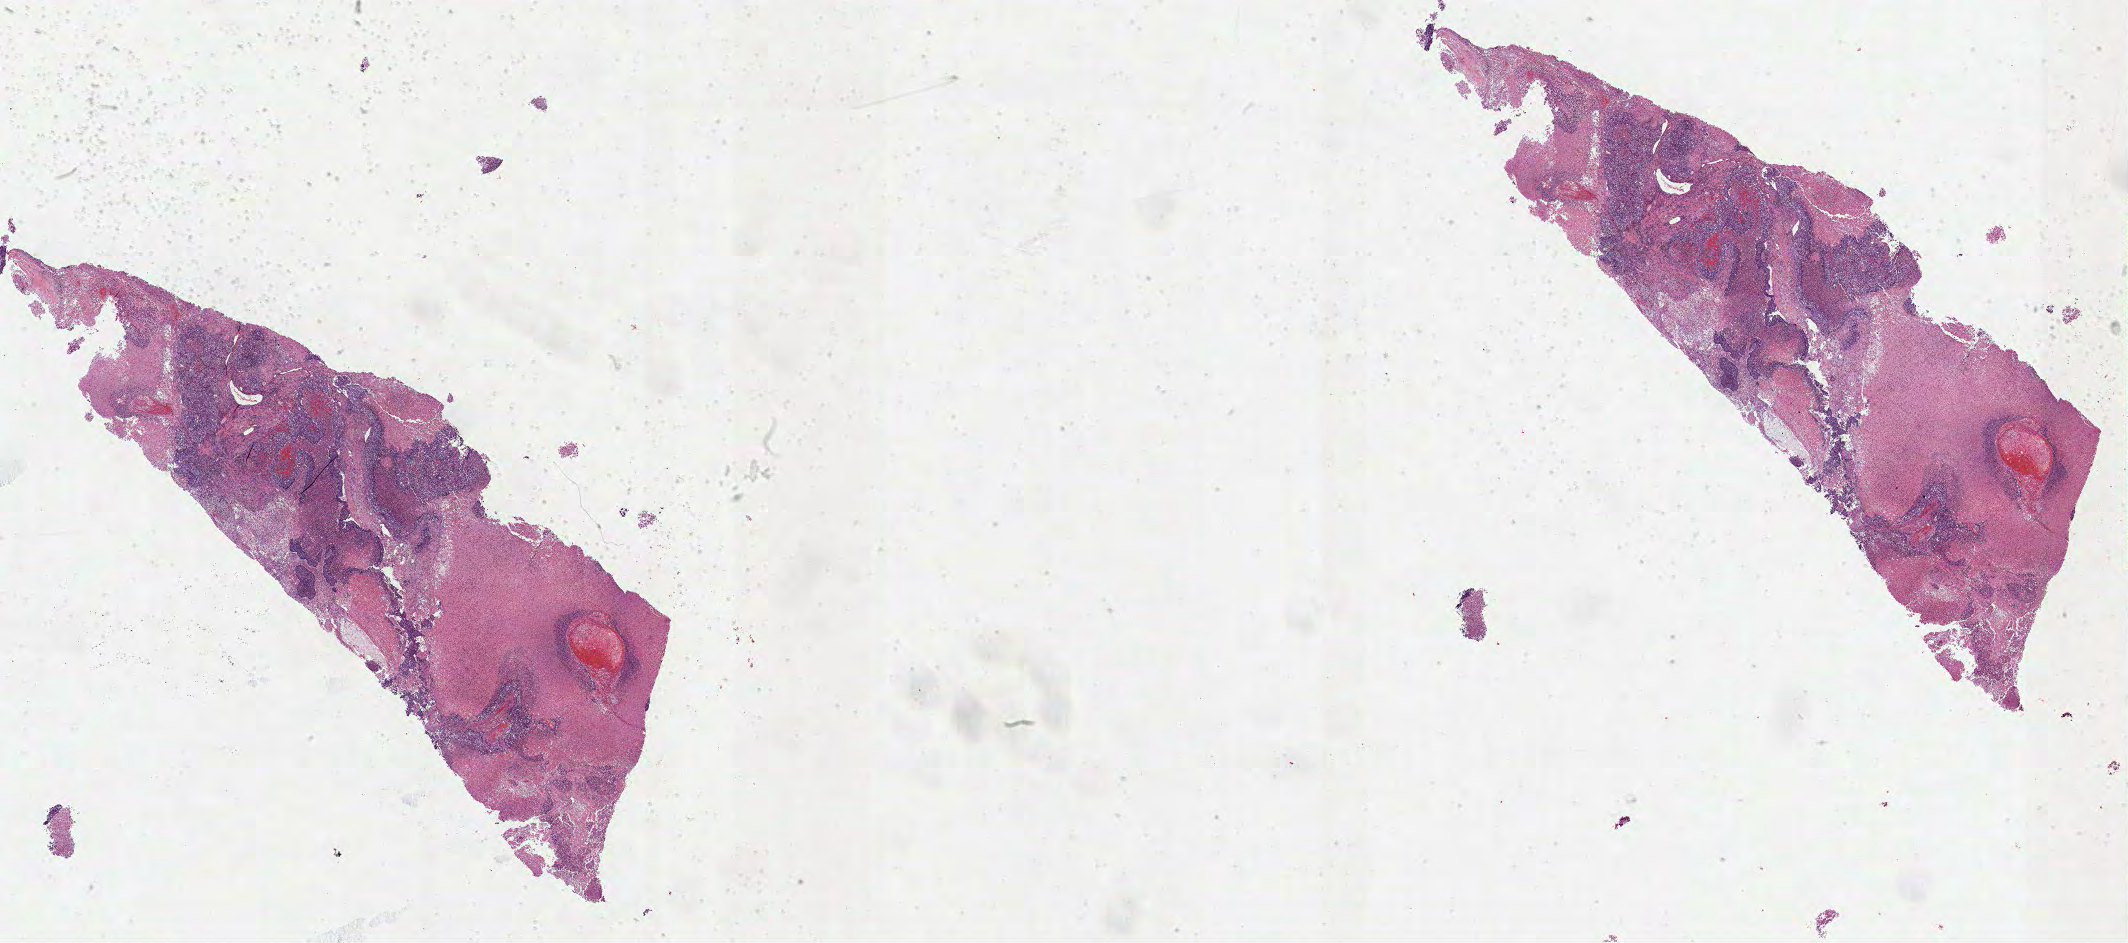
Whole-slide histology image, Hematoxylin and eosin (H&E) stained, whole scanned area (about 34.3 x 15.2 mm, from a 40x scan) shown as a low-resolution overview, formalin-fixed paraffin-embedded (FFPE) diagnostic section, sample: primary tumour, lung. Female patient; age at initial diagnosis 49 years.
TNM: T3 N0 MX. AJCC pathologic stage: IIB (6th edition). Pathologic diagnosis: Adenocarcinoma, NOS (lower lobe, lung).